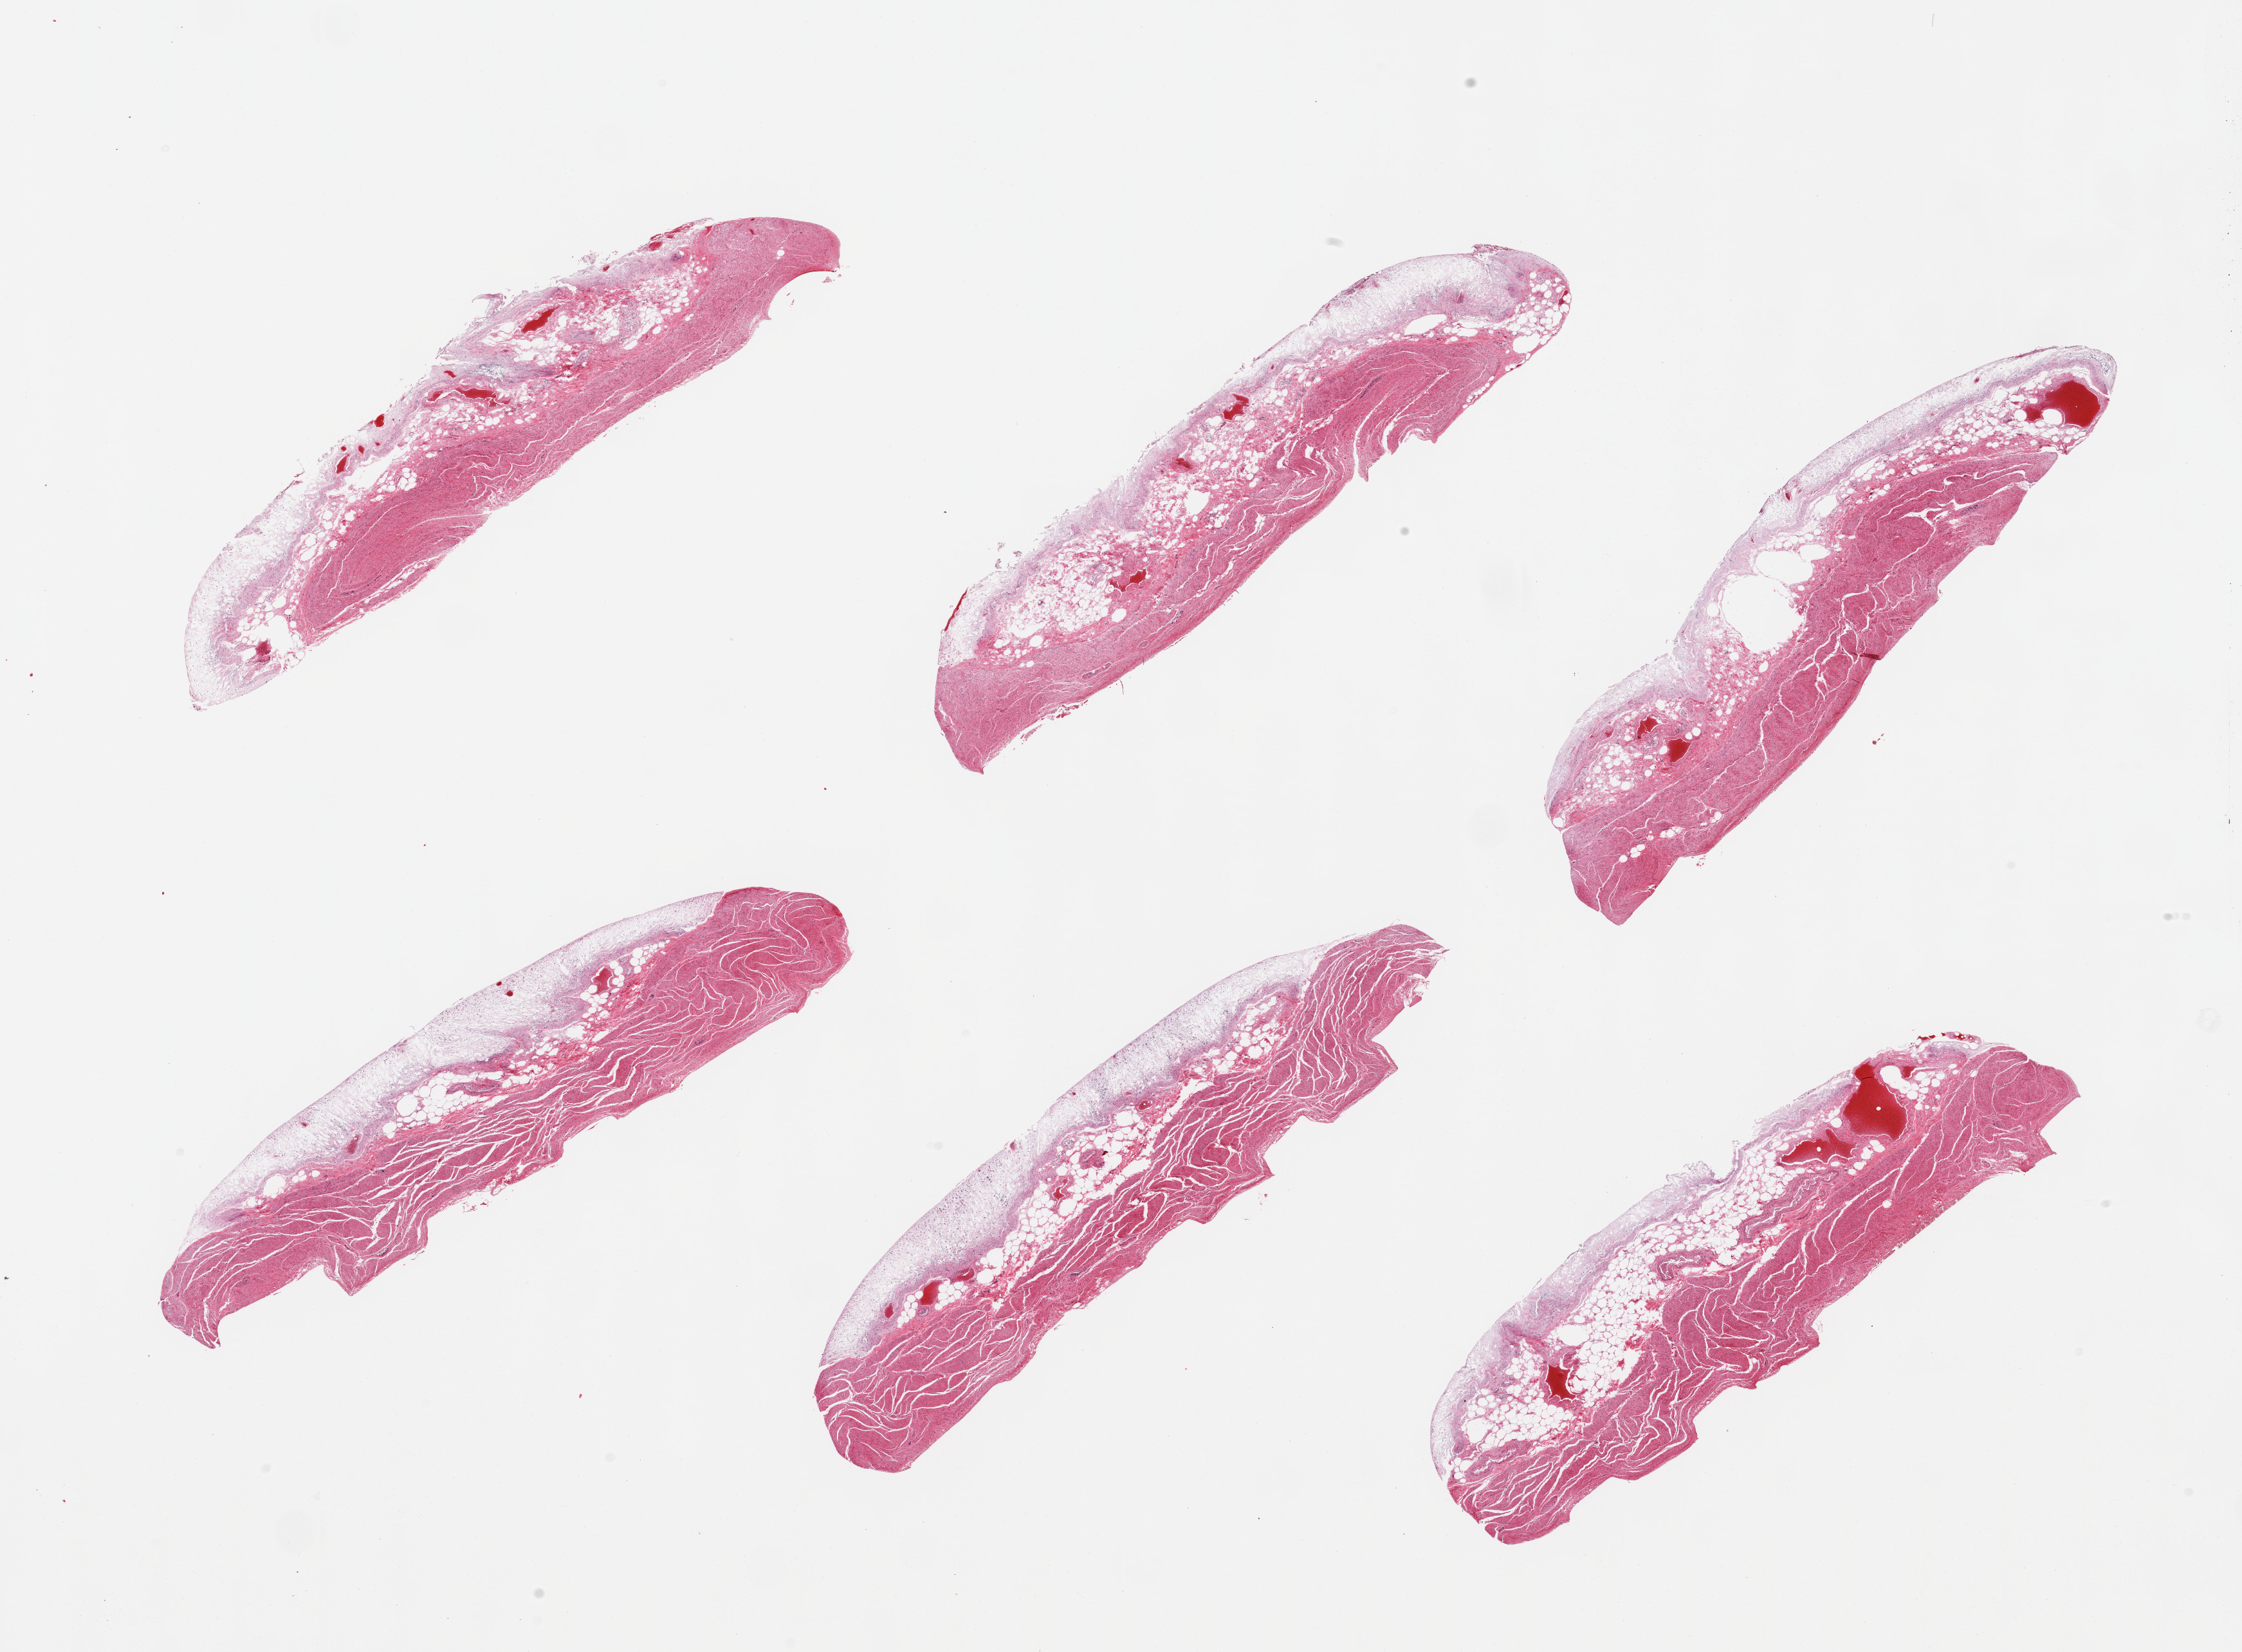
Haematoxylin and eosin whole-slide image, brightfield, a low-resolution overview of the entire scanned area, about 27.6 x 20.3 mm (acquisition: 20x scan), PAXgene-fixed, paraffin-embedded tissue, target tissue: stomach, donor tissue sample. Donor sex: male.
Review note (as recorded): 6 pieces, mucosa up to ~0.9mm, but completely autolyzed.